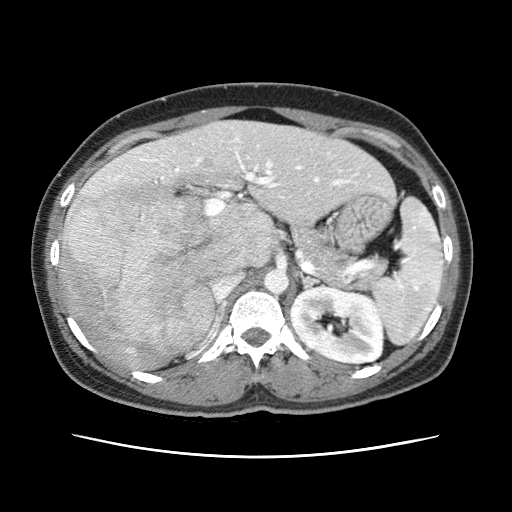
Contrast-enhanced abdominal CT (liver protocol), one axial slice; position 35 of 79 along the scan axis; reconstruction kernel STANDARD; soft-tissue window (W 400 / L 40 HU); 512 × 512 image matrix. Case-level facts recorded for this patient, not image findings: diagnosis: hepatocellular carcinoma (patient treated with transarterial chemoembolisation; whether this scan precedes or follows treatment is not stated here); TNM stage (as recorded): Stage-I; Child-Pugh class: A; tumour differentiation: moderately differentiated; tumour nodularity: uninodular.
Structures marked on this image (semi-automatically segmented with operator editing):
- abdominal aorta: bounding box [x1, y1, x2, y2] px = [265, 270, 289, 294]
- liver parenchyma outside the tumour (the mass and vessels are separate outlines, so this box may not span the whole liver): [62, 120, 394, 362]
- mass: [58, 180, 221, 372]
- liver vessels: [108, 137, 370, 216]